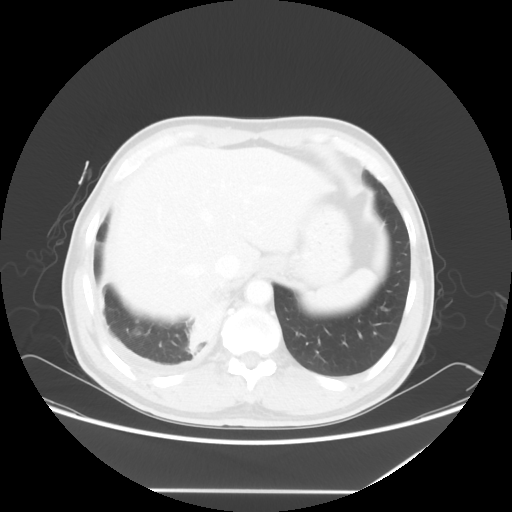
Chest CT, one axial slice. Slice 11 of 60 in the series (ordered by position). Lung window (W 1500 / L -600 HU). 512 × 512 image matrix, field of view 419 × 419 mm. Male patient, age 48 years. Case-level facts recorded for this patient, not image findings: clinical TNM (as recorded): T3 N3 M1a.
Outlined on this slice (rectangle marked by the reading radiologist):
- lung tumour (recorded histology: squamous cell carcinoma): box from (x=184, y=289) to (x=227, y=356) px